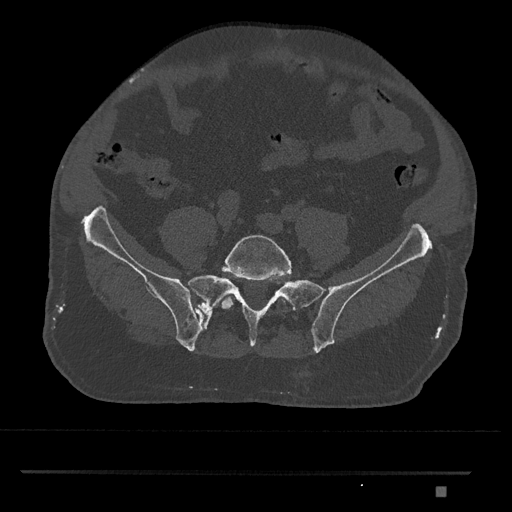
CT including the spine, one axial slice. Slice 527 of 1134 in the series (ordered by position). Reconstruction kernel Br40s/3. Bone window (W 1800 / L 400 HU). 0.5 mm slice thickness. 512 × 512 image matrix, field of view 429 × 429 mm. Male patient, age 65 years. From the clinical record (not read from this slice): primary cancer: prostate.
Outlined on this slice (semi-automatic segmentation, software-assisted and operator-edited):
- L5 vertebra: bounding box <221,234,292,311> (left, top, right, bottom; pixels)